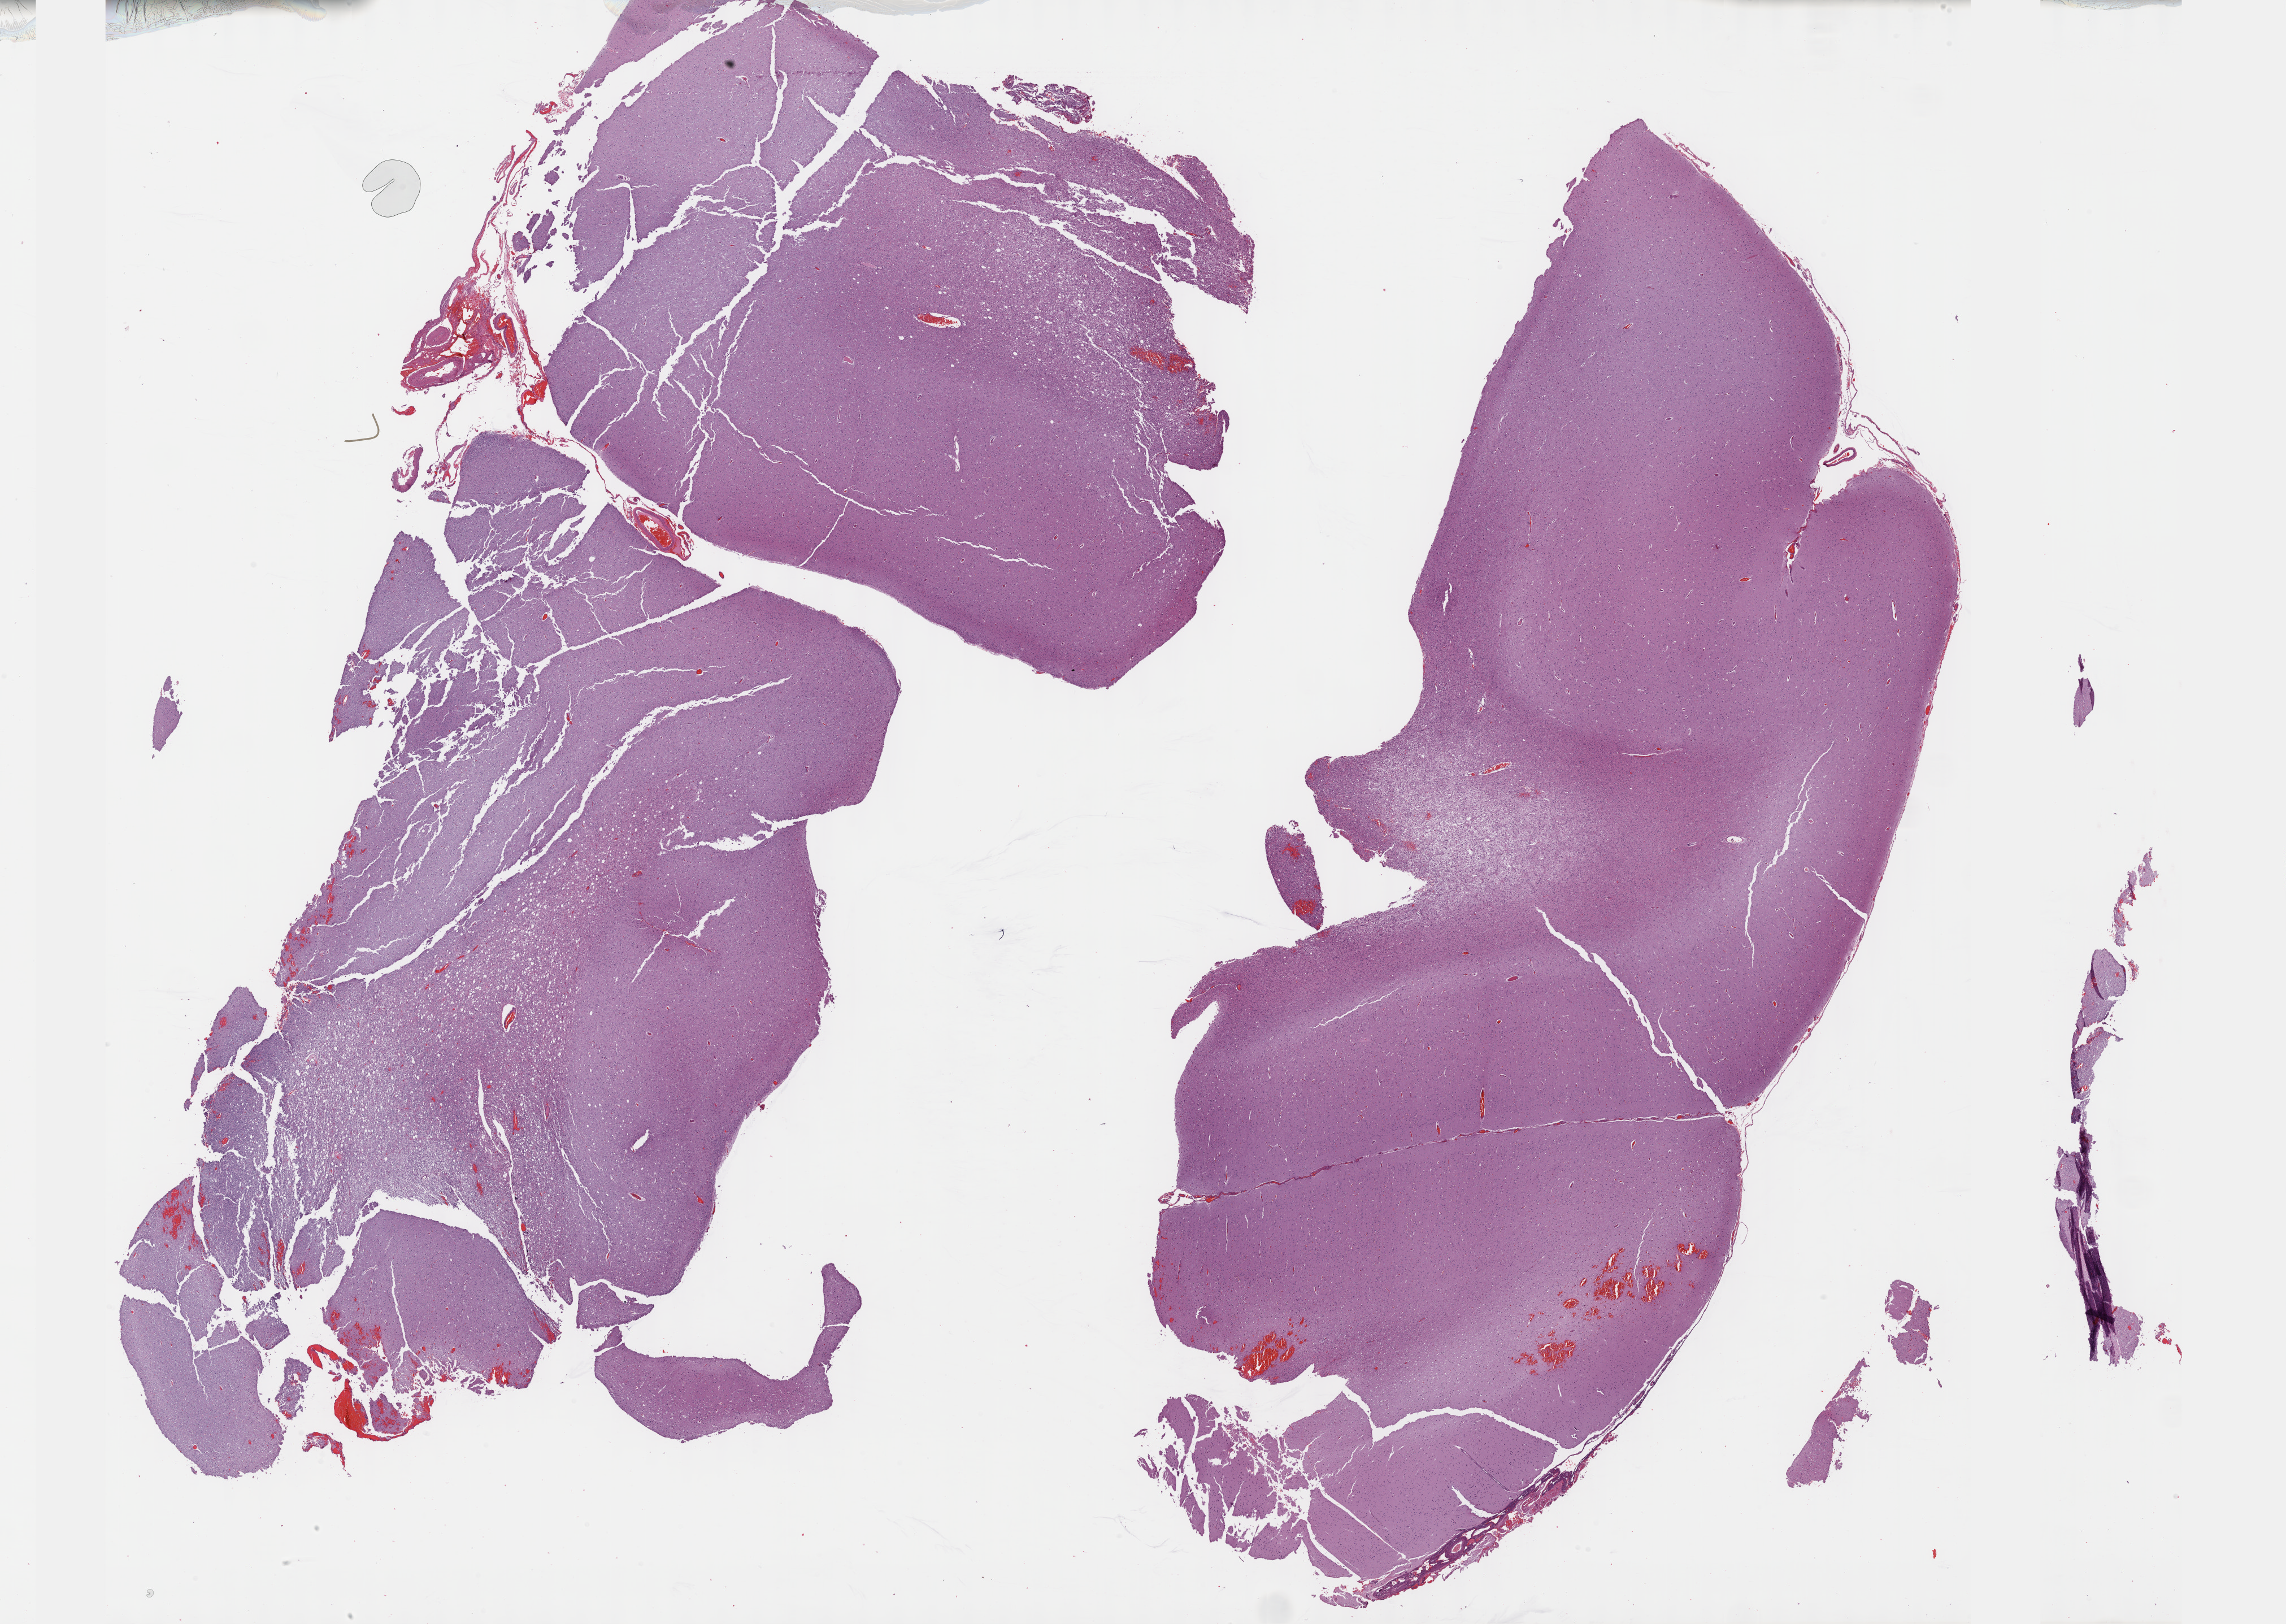
Whole-slide histology image, Hematoxylin and eosin (H&E) stained — a low-resolution overview of the entire scanned area, about 32.7 x 23.2 mm; formalin-fixed paraffin-embedded (FFPE) diagnostic section; sample: primary tumour, brain. Patient: male, age at initial diagnosis 35 years. Histologic grade: G3 (poorly differentiated).
Pathologic diagnosis: Oligodendroglioma, anaplastic. Laterality: left.